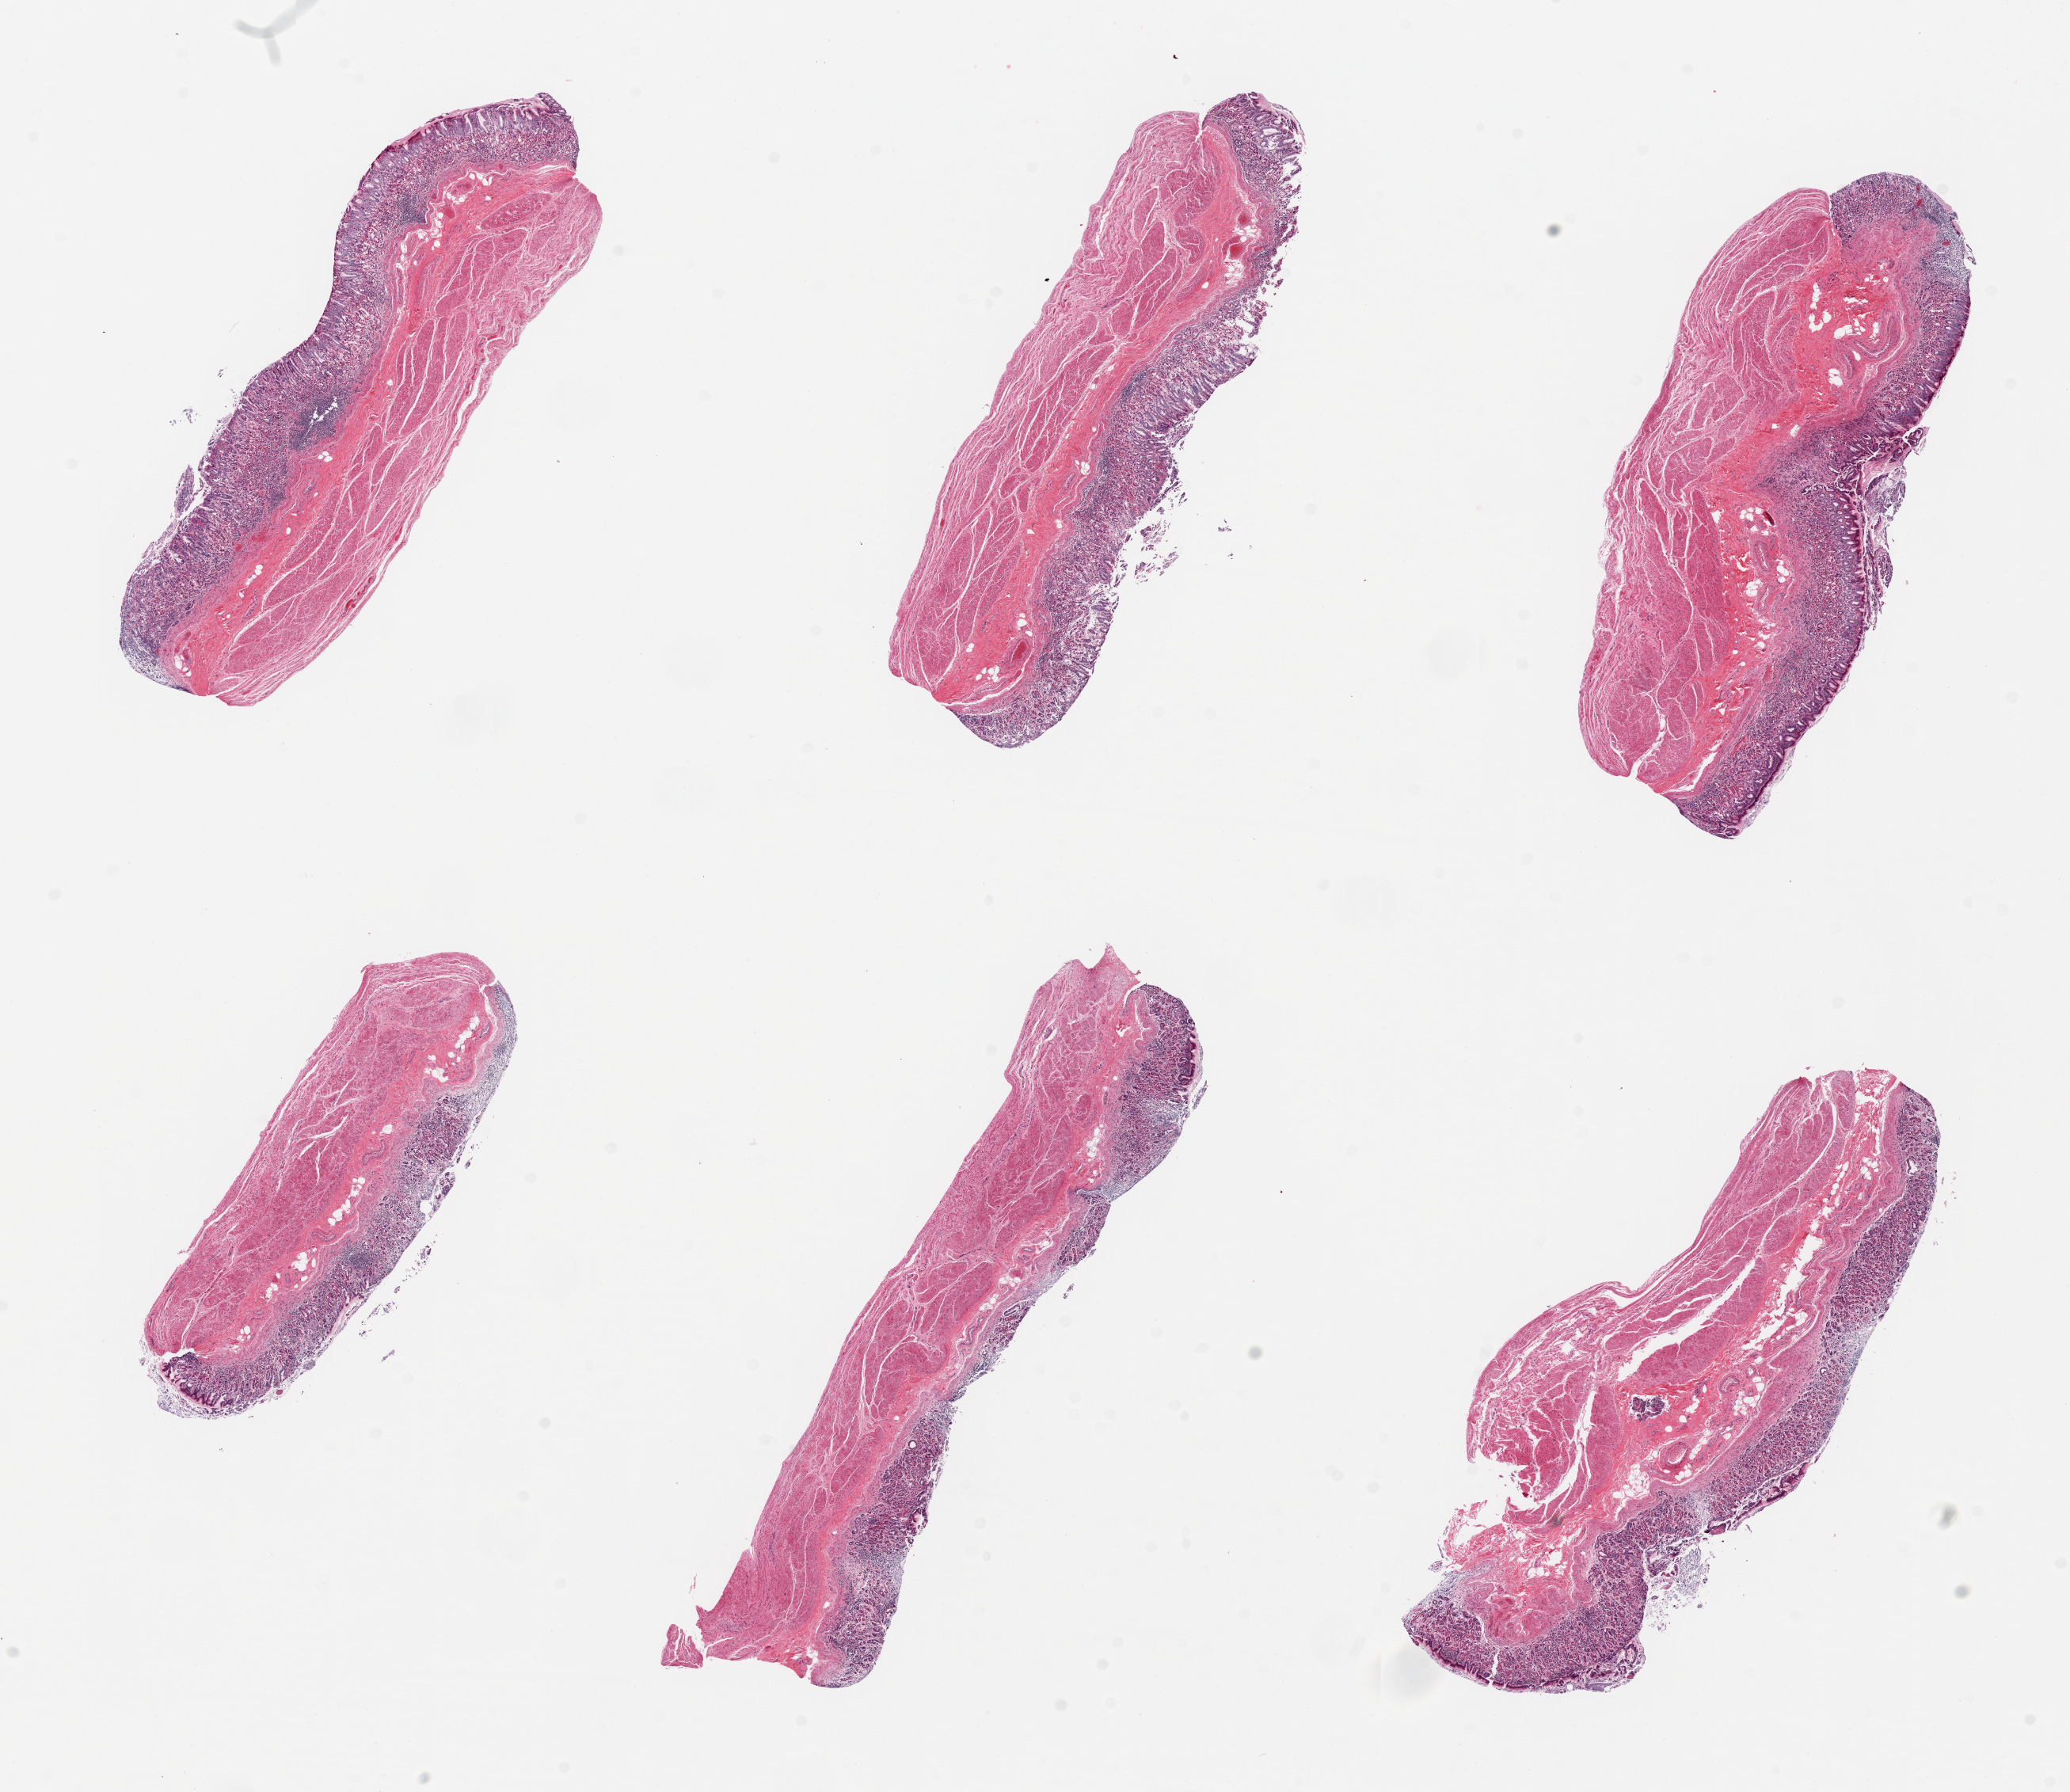
Digitized H&E-stained section — shown as a low-resolution overview of the whole scanned area (about 20.7 x 17.9 mm, acquisition: 20x scan); PAXgene-fixed paraffin-embedded (PFPE) section; section of stomach (target tissue); donor tissue sample. Donor: female.
Pathologist's review note for this sample: 6 pieces; moderate chronic gastritis.